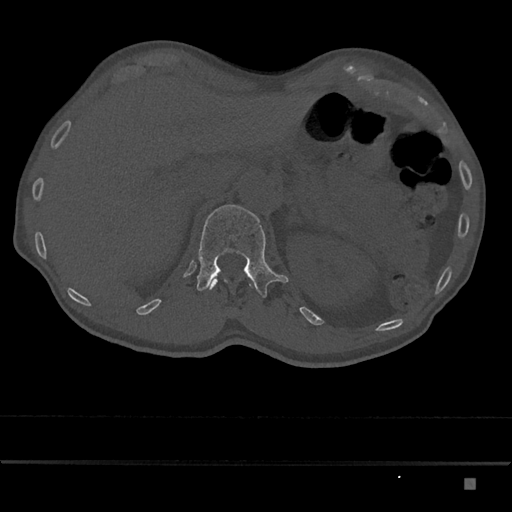
CT including the spine, one axial slice. Position 563 of 797 along the scan axis. 120 kVp. Bone window (W 1800 / L 400 HU). 512 × 512 image matrix. Male patient, age 72 years. From the clinical record (not read from this slice): primary cancer: prostate.
Structures marked on this image (semi-automatically segmented with operator editing):
- L1 vertebra: bounding box (x1, y1, x2, y2) in pixels: (197, 205, 289, 298)
- T12 vertebra: (206, 277, 254, 289)